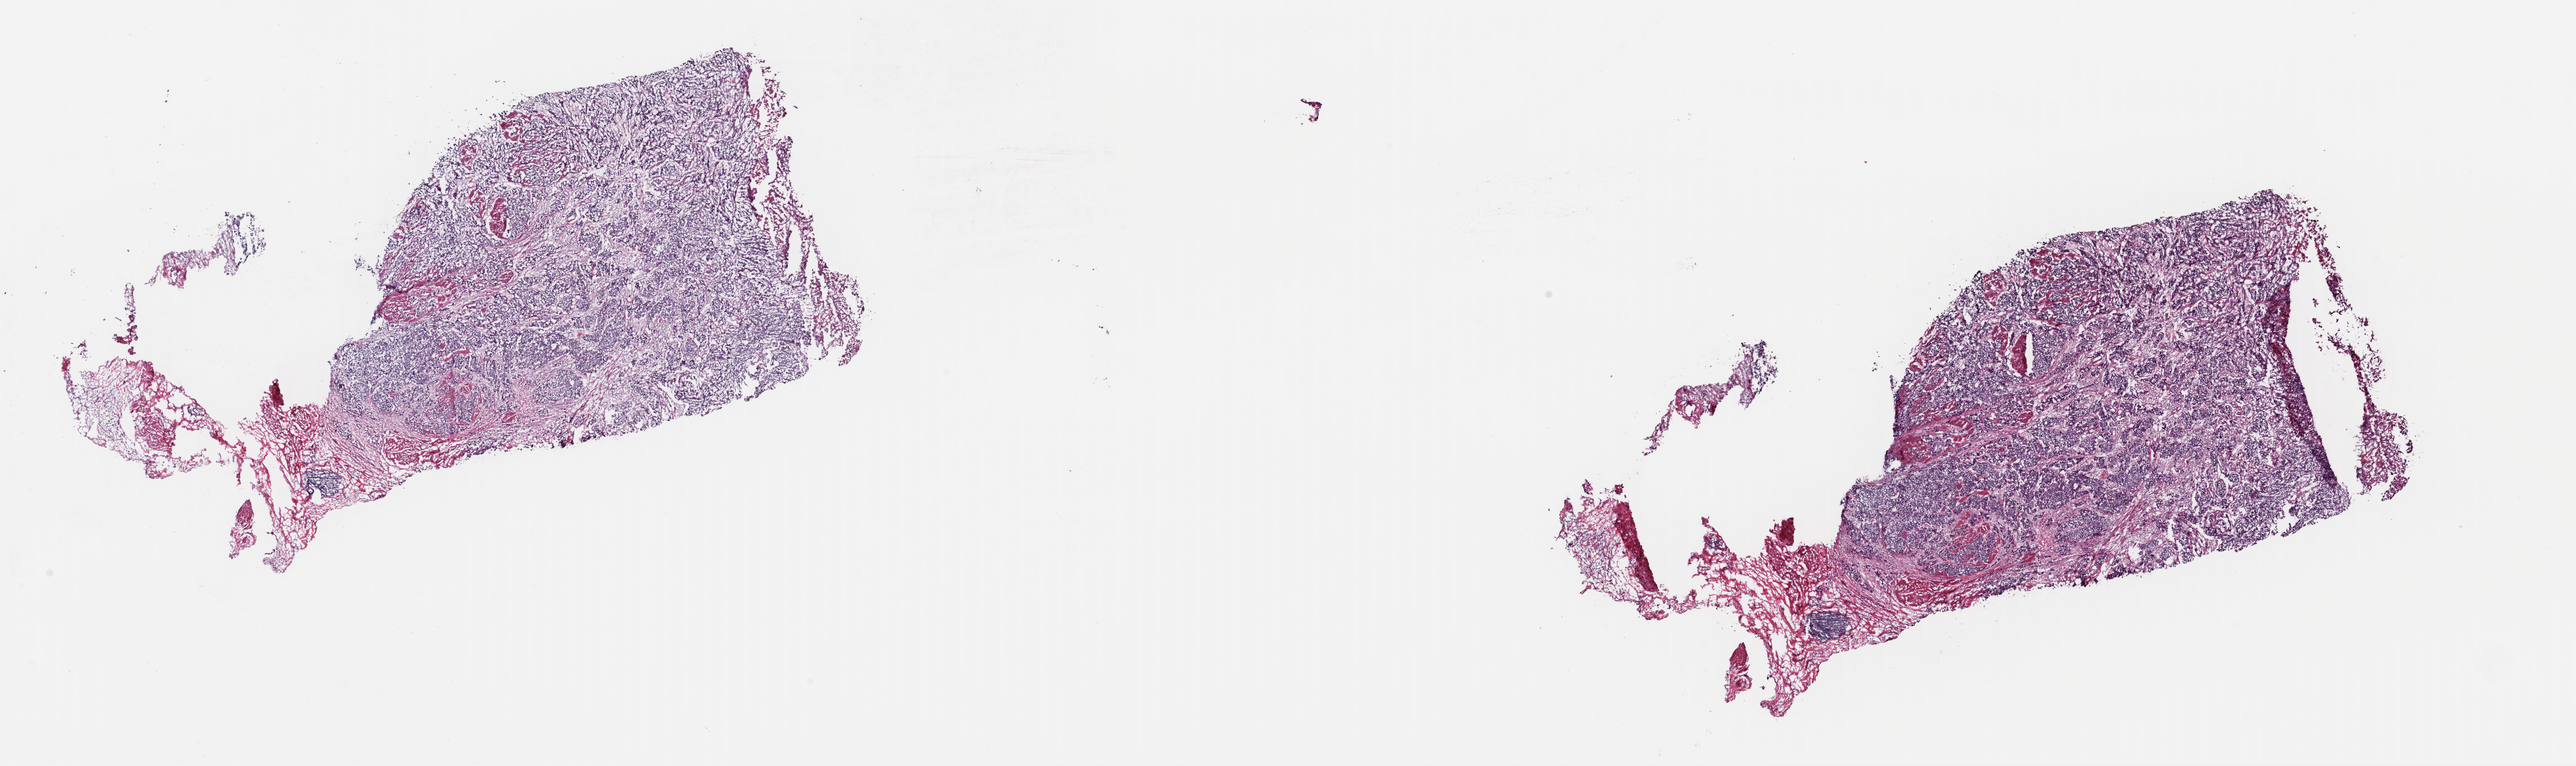
H&E-stained whole-slide image, low-resolution overview of the scanned area, about 30.8 x 9.2 mm (acquisition: 40x scan); frozen section from the top of the tissue portion; primary tumour sample from the bladder. Female, age 79 years at initial diagnosis. Histologic grade: high grade. Composition of this section per pathologist review: tumour cells 80%, tumour nuclei 90%, normal cells 0%, stromal cells 20%, necrosis 0%. Infiltration values recorded for this section: lymphocyte infiltration 0%, monocyte infiltration 0%, neutrophil infiltration 0%.
Pathologic diagnosis: Transitional cell carcinoma (lateral wall of bladder). TNM: T3 N2 M0. Lymph nodes positive (case pathology): 2 of 5 examined. AJCC pathologic stage: IV (6th edition).